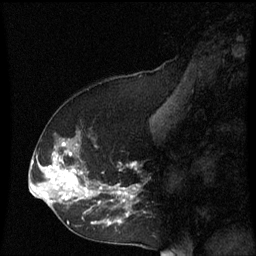
Breast MRI (dynamic contrast-enhanced), one sagittal slice; slice 28 of 60 in the series (ordered by position); dynamic contrast-enhanced series, image 2 of 3 at this slice position (ordered by acquisition); 1.5 T; TE 4.2 ms, TR 8.9 ms; 2 mm slice thickness; 256 × 256 image matrix, field of view 200 × 200 mm. Patient: female, 53 years. Case-level facts recorded for this patient, not image findings: setting: breast cancer imaged before/during neoadjuvant chemotherapy; receptor status: HR-positive, HER2-negative.
Annotated regions visible in this slice (semi-automatic segmentation, software-assisted and operator-edited):
- analysis volume of interest (the breast-tissue region the enhancement analysis was run in; not a lesion): bounding box [x1, y1, x2, y2] px = [38, 128, 147, 231]
- tumour enhancement mask (voxels above the 70 % enhancement threshold inside the analysis volume of interest): [48, 142, 135, 225]